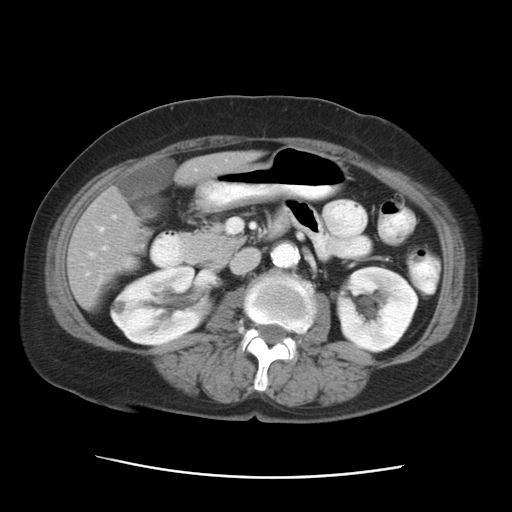
Contrast-enhanced abdominal CT, one axial slice; position 11 of 29 along the scan axis; 120 kVp; intravenous contrast given; soft-tissue window (W 400 / L 40 HU); 7.5 mm slice thickness; 512 × 512 image matrix. Female patient, age 64 years. From the clinical record (not read from this slice): diagnosis: colorectal cancer liver metastases, imaged before liver resection; multiple liver metastases: no; largest metastasis: 2.5 cm; chemotherapy before resection: no.
Structures marked on this image (manually delineated by an expert):
- hepatic veins: box from (x=99, y=227) to (x=104, y=231) px
- liver: (x=67, y=151)–(x=257, y=307)
- planned liver remnant (the part of the liver to remain after resection): (x=67, y=151)–(x=257, y=306)
- portal vein (with intrahepatic branches): (x=226, y=220)–(x=237, y=234)